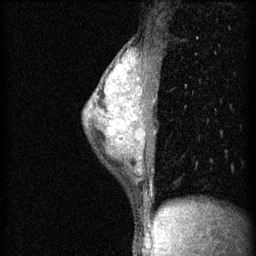
Breast MRI (dynamic contrast-enhanced), one sagittal slice. Position 39 of 60 along the scan axis. 3 images stored at this slice position (order not interpretable as contrast timing). 1.5 T. TE 4.2 ms, TR 11 ms. 2 mm slice thickness. 256 × 256 image matrix, field of view 180 × 180 mm. Female patient, age 40 years.
Structures marked on this image (semi-automatic segmentation, software-assisted and operator-edited):
- analysis volume of interest (the breast-tissue region the enhancement analysis was run in; not a lesion): bounding box [x1, y1, x2, y2] px = [83, 50, 155, 189]
- tumour enhancement mask (voxels above the 70 % enhancement threshold inside the analysis volume of interest): [114, 94, 142, 127]